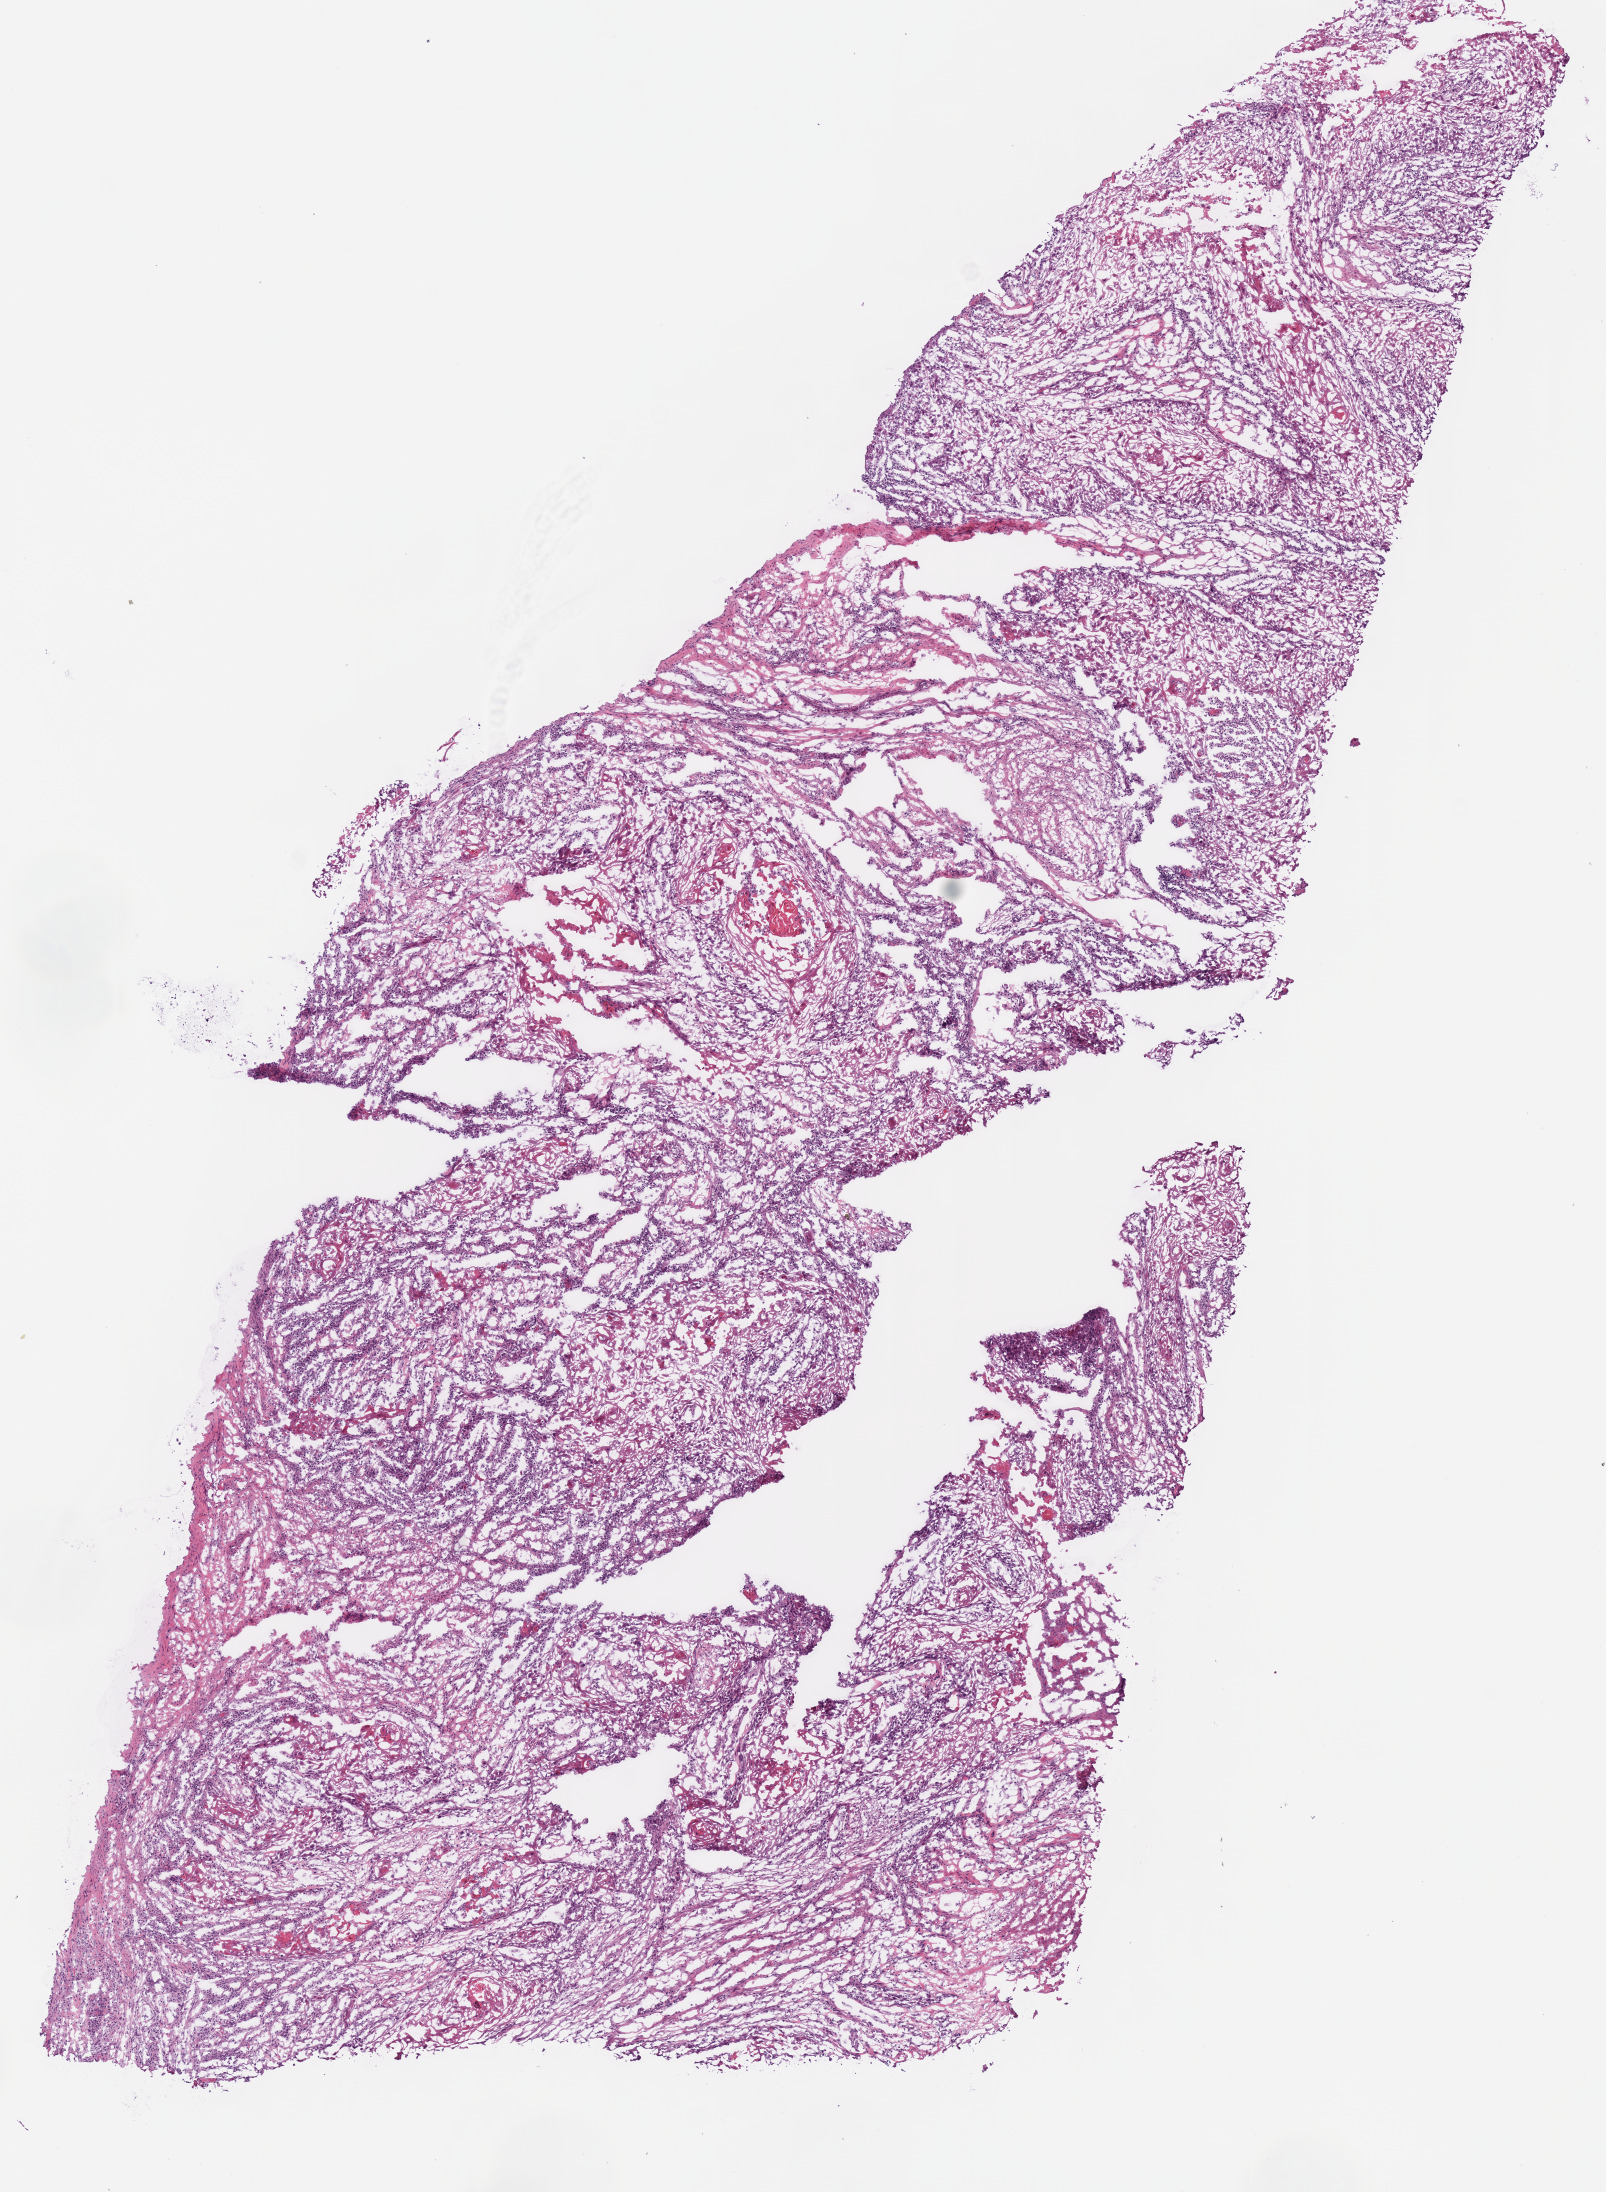
Whole-slide histology image, Hematoxylin and eosin (H&E) stained, shown as a low-resolution overview of the whole scanned area (about 6.3 x 8.6 mm). Frozen section from the top of the tissue portion. Sample: primary tumour, head and neck. Male, age 49 years at initial diagnosis. Histologic grade: G3 (poorly differentiated). Pathologist review of this section (percent, as recorded): tumour cells 72%, tumour nuclei 60%, normal cells 0%, stromal cells 20%, necrosis 8%.
Pathologic diagnosis: Squamous cell carcinoma, NOS (larynx, NOS). AJCC pathologic stage: IVA.